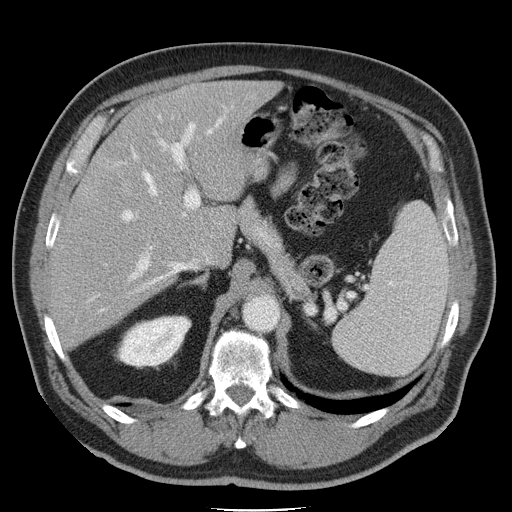
Contrast-enhanced abdominal CT, one axial slice; 120 kVp; intravenous contrast given; soft-tissue window (W 400 / L 40 HU); 5 mm slice thickness; 512 × 512 image matrix, field of view 386 × 386 mm. Male patient, age 65 years. From the clinical record (not read from this slice): diagnosis: colorectal cancer liver metastases, imaged before liver resection; multiple liver metastases: yes; largest metastasis: 4.9 cm.
Annotated regions visible in this slice (manually delineated by an expert):
- hepatic veins: bounding box [x1, y1, x2, y2] px = [83, 114, 227, 314]
- liver: [57, 81, 272, 343]
- planned liver remnant (the part of the liver to remain after resection): [103, 81, 272, 255]
- portal vein (with intrahepatic branches): [119, 122, 201, 283]